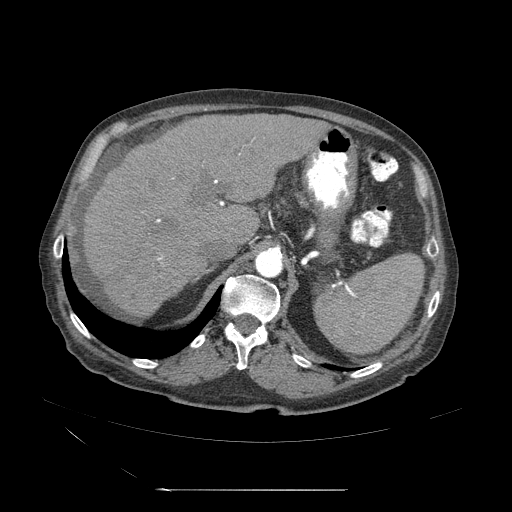
Contrast-enhanced abdominal CT (liver protocol), one axial slice. Slice 33 of 71 in the series (ordered by position). Reconstruction kernel STANDARD. 120 kVp. Soft-tissue window (W 400 / L 40 HU). 2.5 mm slice thickness. 512 × 512 image matrix, field of view 440 × 440 mm. Case-level facts recorded for this patient, not image findings: diagnosis: hepatocellular carcinoma (patient treated with transarterial chemoembolisation; whether this scan precedes or follows treatment is not stated here); TNM stage (as recorded): Stage-II; Child-Pugh class: A; tumour nodularity: multinodular; tumour size: 1 cm.
Annotated regions visible in this slice (semi-automatically segmented with operator editing):
- abdominal aorta: bounding box [x1, y1, x2, y2] px = [255, 248, 284, 277]
- liver parenchyma outside the tumour (the mass and vessels are separate outlines, so this box may not span the whole liver): [79, 115, 329, 323]
- liver vessels: [136, 161, 236, 289]